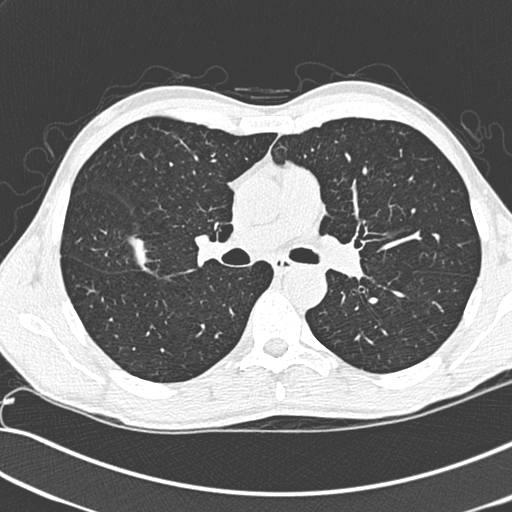
Low-dose screening chest CT, one axial slice. Slice 183 of 281 in the series (ordered by position). 120 kVp. Lung window (W 1500 / L -600 HU). 1.3 mm slice thickness. 512 × 512 image matrix, field of view 341 × 341 mm.
Annotated regions visible in this slice (manually delineated by an expert):
- lesion 1 (tumor, upper lobe of right lung): bounding box <129,236,152,273> (left, top, right, bottom; pixels)